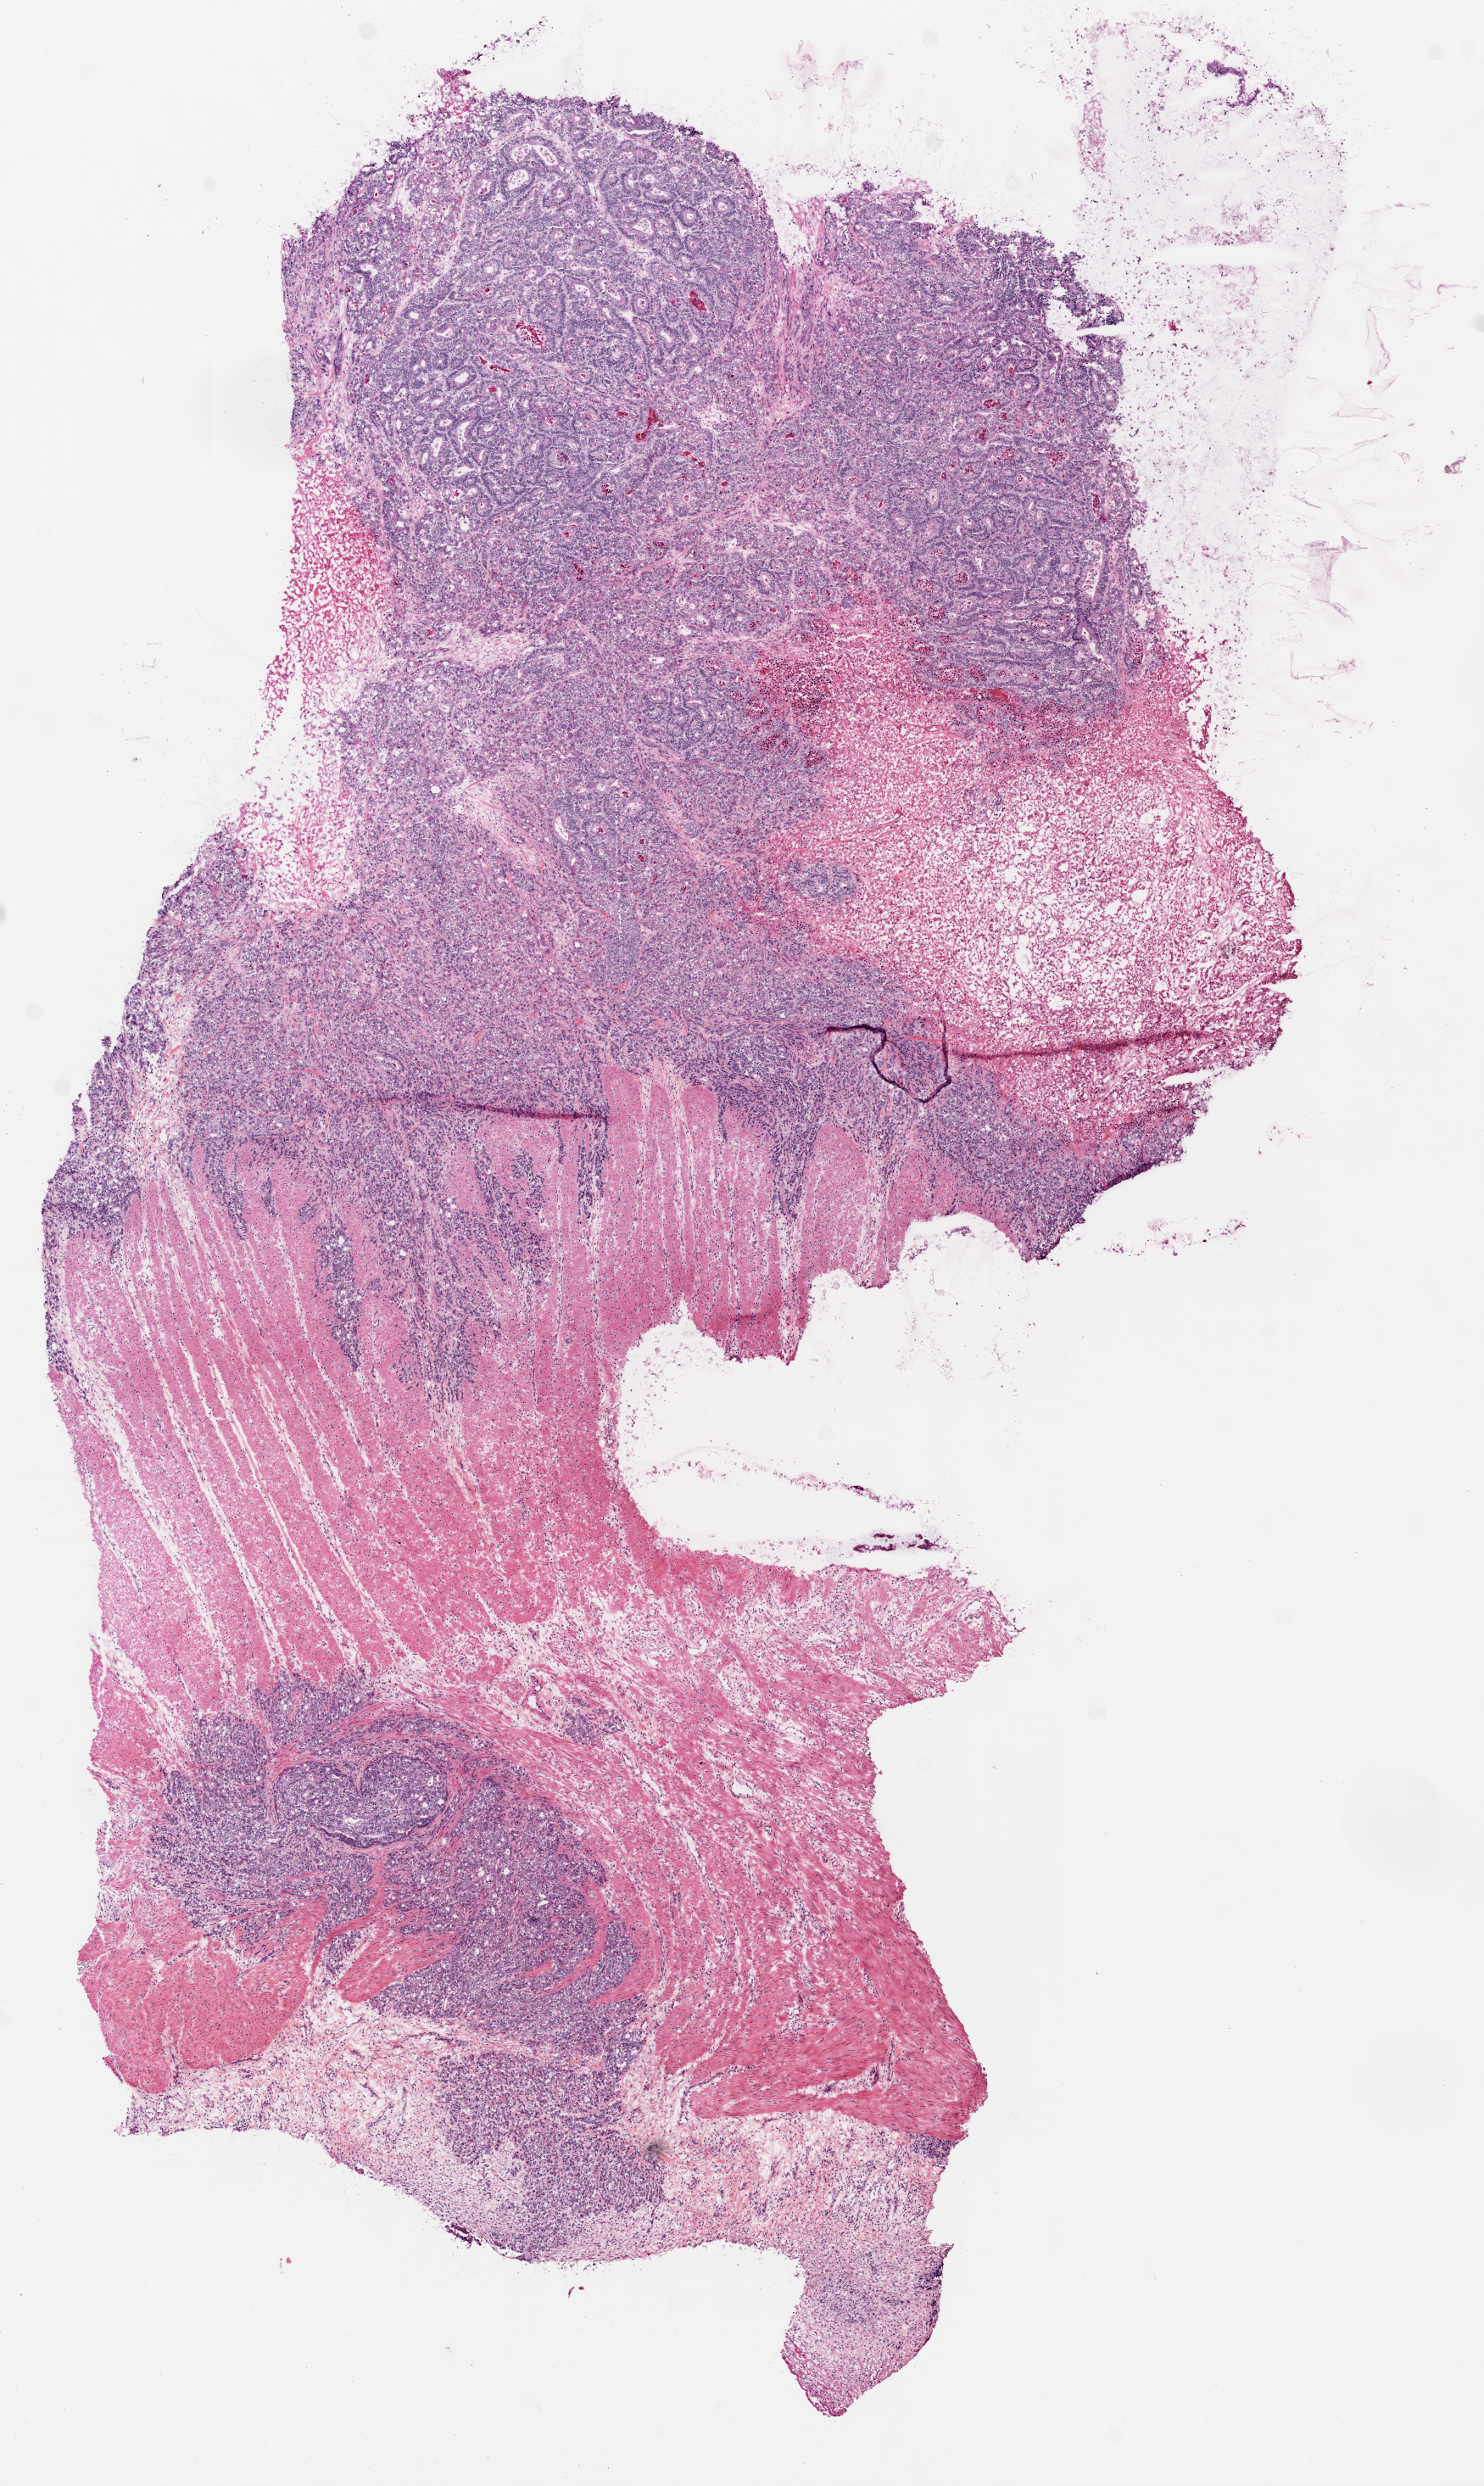
Digitized Hematoxylin and eosin (H&E) stained tissue section (whole slide) — a low-resolution overview of the entire scanned area, about 7.0 x 11.8 mm. Frozen section. Primary tumour sample from the colon. Patient: female, age at initial diagnosis 59 years. Slide review estimates, as recorded: tumour cells 75%, tumour nuclei 80%.
Histologic diagnosis: Adenocarcinoma, NOS.